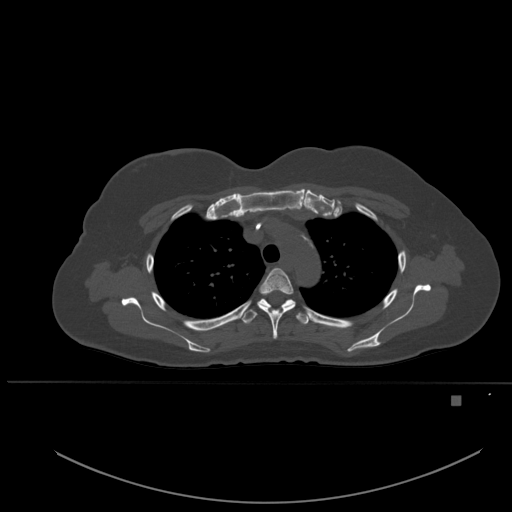
CT including the spine, one axial slice. Position 388 of 651 along the scan axis. Bone window (W 1800 / L 400 HU). 1.5 mm slice thickness. 512 × 512 image matrix, field of view 443 × 443 mm. Patient: female, 49 years. From the clinical record (not read from this slice): primary cancer: breast; vertebrae with lytic lesions (as recorded): L3, T12, L4.
Annotated regions visible in this slice (semi-automatically segmented with operator editing):
- T3 vertebra: box from (x=257, y=268) to (x=295, y=339) px
- T4 vertebra: (x=241, y=298)–(x=309, y=325)